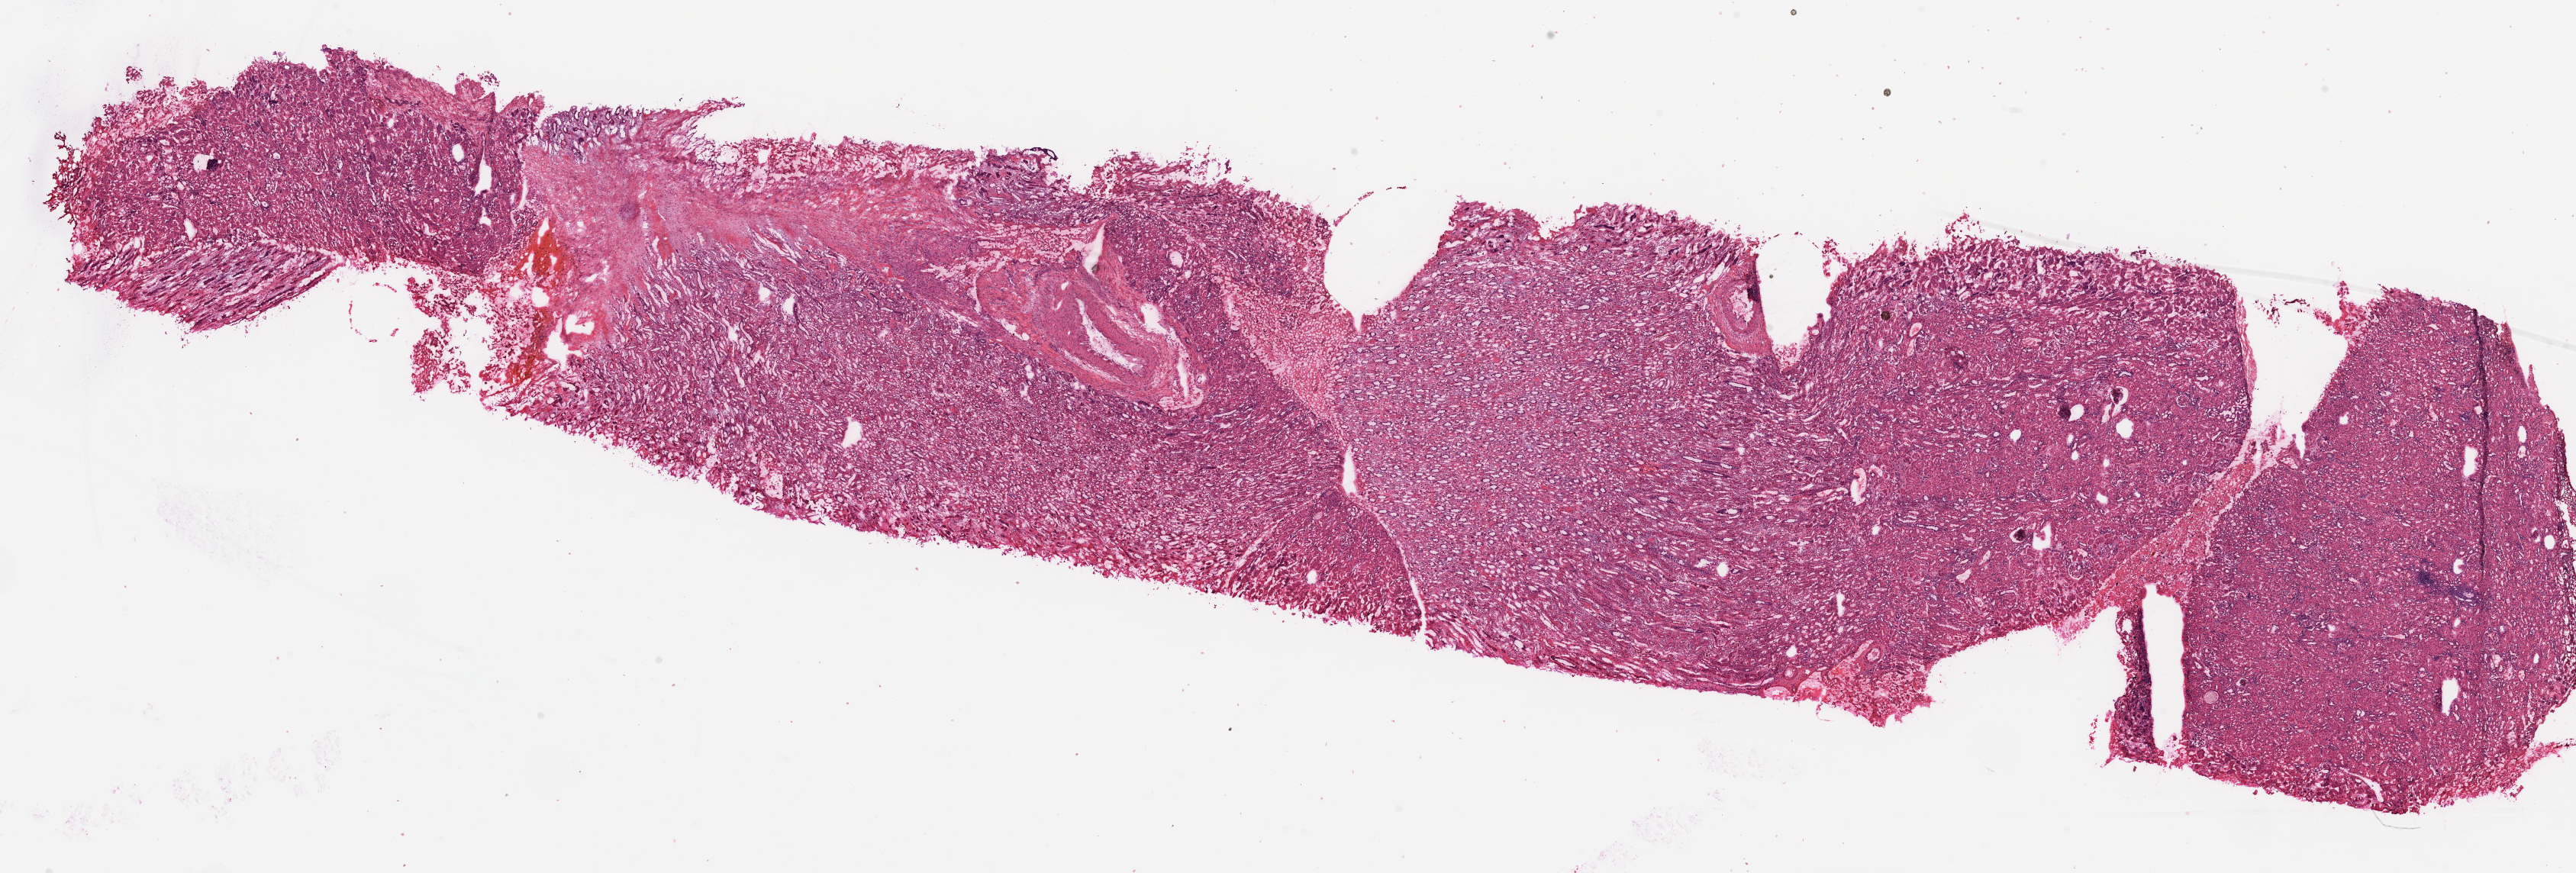
H&E whole-slide image — a low-resolution overview of the entire scanned area, about 27.1 x 9.2 mm (slide scanned at 20x). Frozen section from the top of the tissue portion. Solid tissue normal (non-tumour tissue) sample from the kidney. Male patient; age at initial diagnosis 48 years.
This section: solid tissue normal (non-tumour) sample from the same patient. Patient diagnosis: Clear cell adenocarcinoma, NOS.